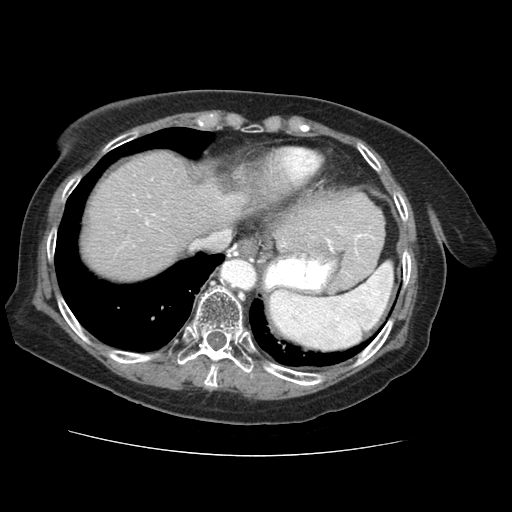
Contrast-enhanced abdominal CT (liver protocol), one axial slice; position 55 of 73 along the scan axis; reconstruction kernel STANDARD; soft-tissue window (W 400 / L 40 HU); 2.5 mm slice thickness; 512 × 512 image matrix, field of view 360 × 360 mm. Case-level facts recorded for this patient, not image findings: diagnosis: hepatocellular carcinoma (patient treated with transarterial chemoembolisation; whether this scan precedes or follows treatment is not stated here); TNM stage (as recorded): Stage-IVB; Child-Pugh class: A; tumour differentiation: well differentiated.
Outlined on this slice (semi-automatically segmented with operator editing):
- liver parenchyma outside the tumour (the mass and vessels are separate outlines, so this box may not span the whole liver): box from (x=84, y=152) to (x=246, y=280) px
- liver vessels: (x=136, y=209)–(x=155, y=225)